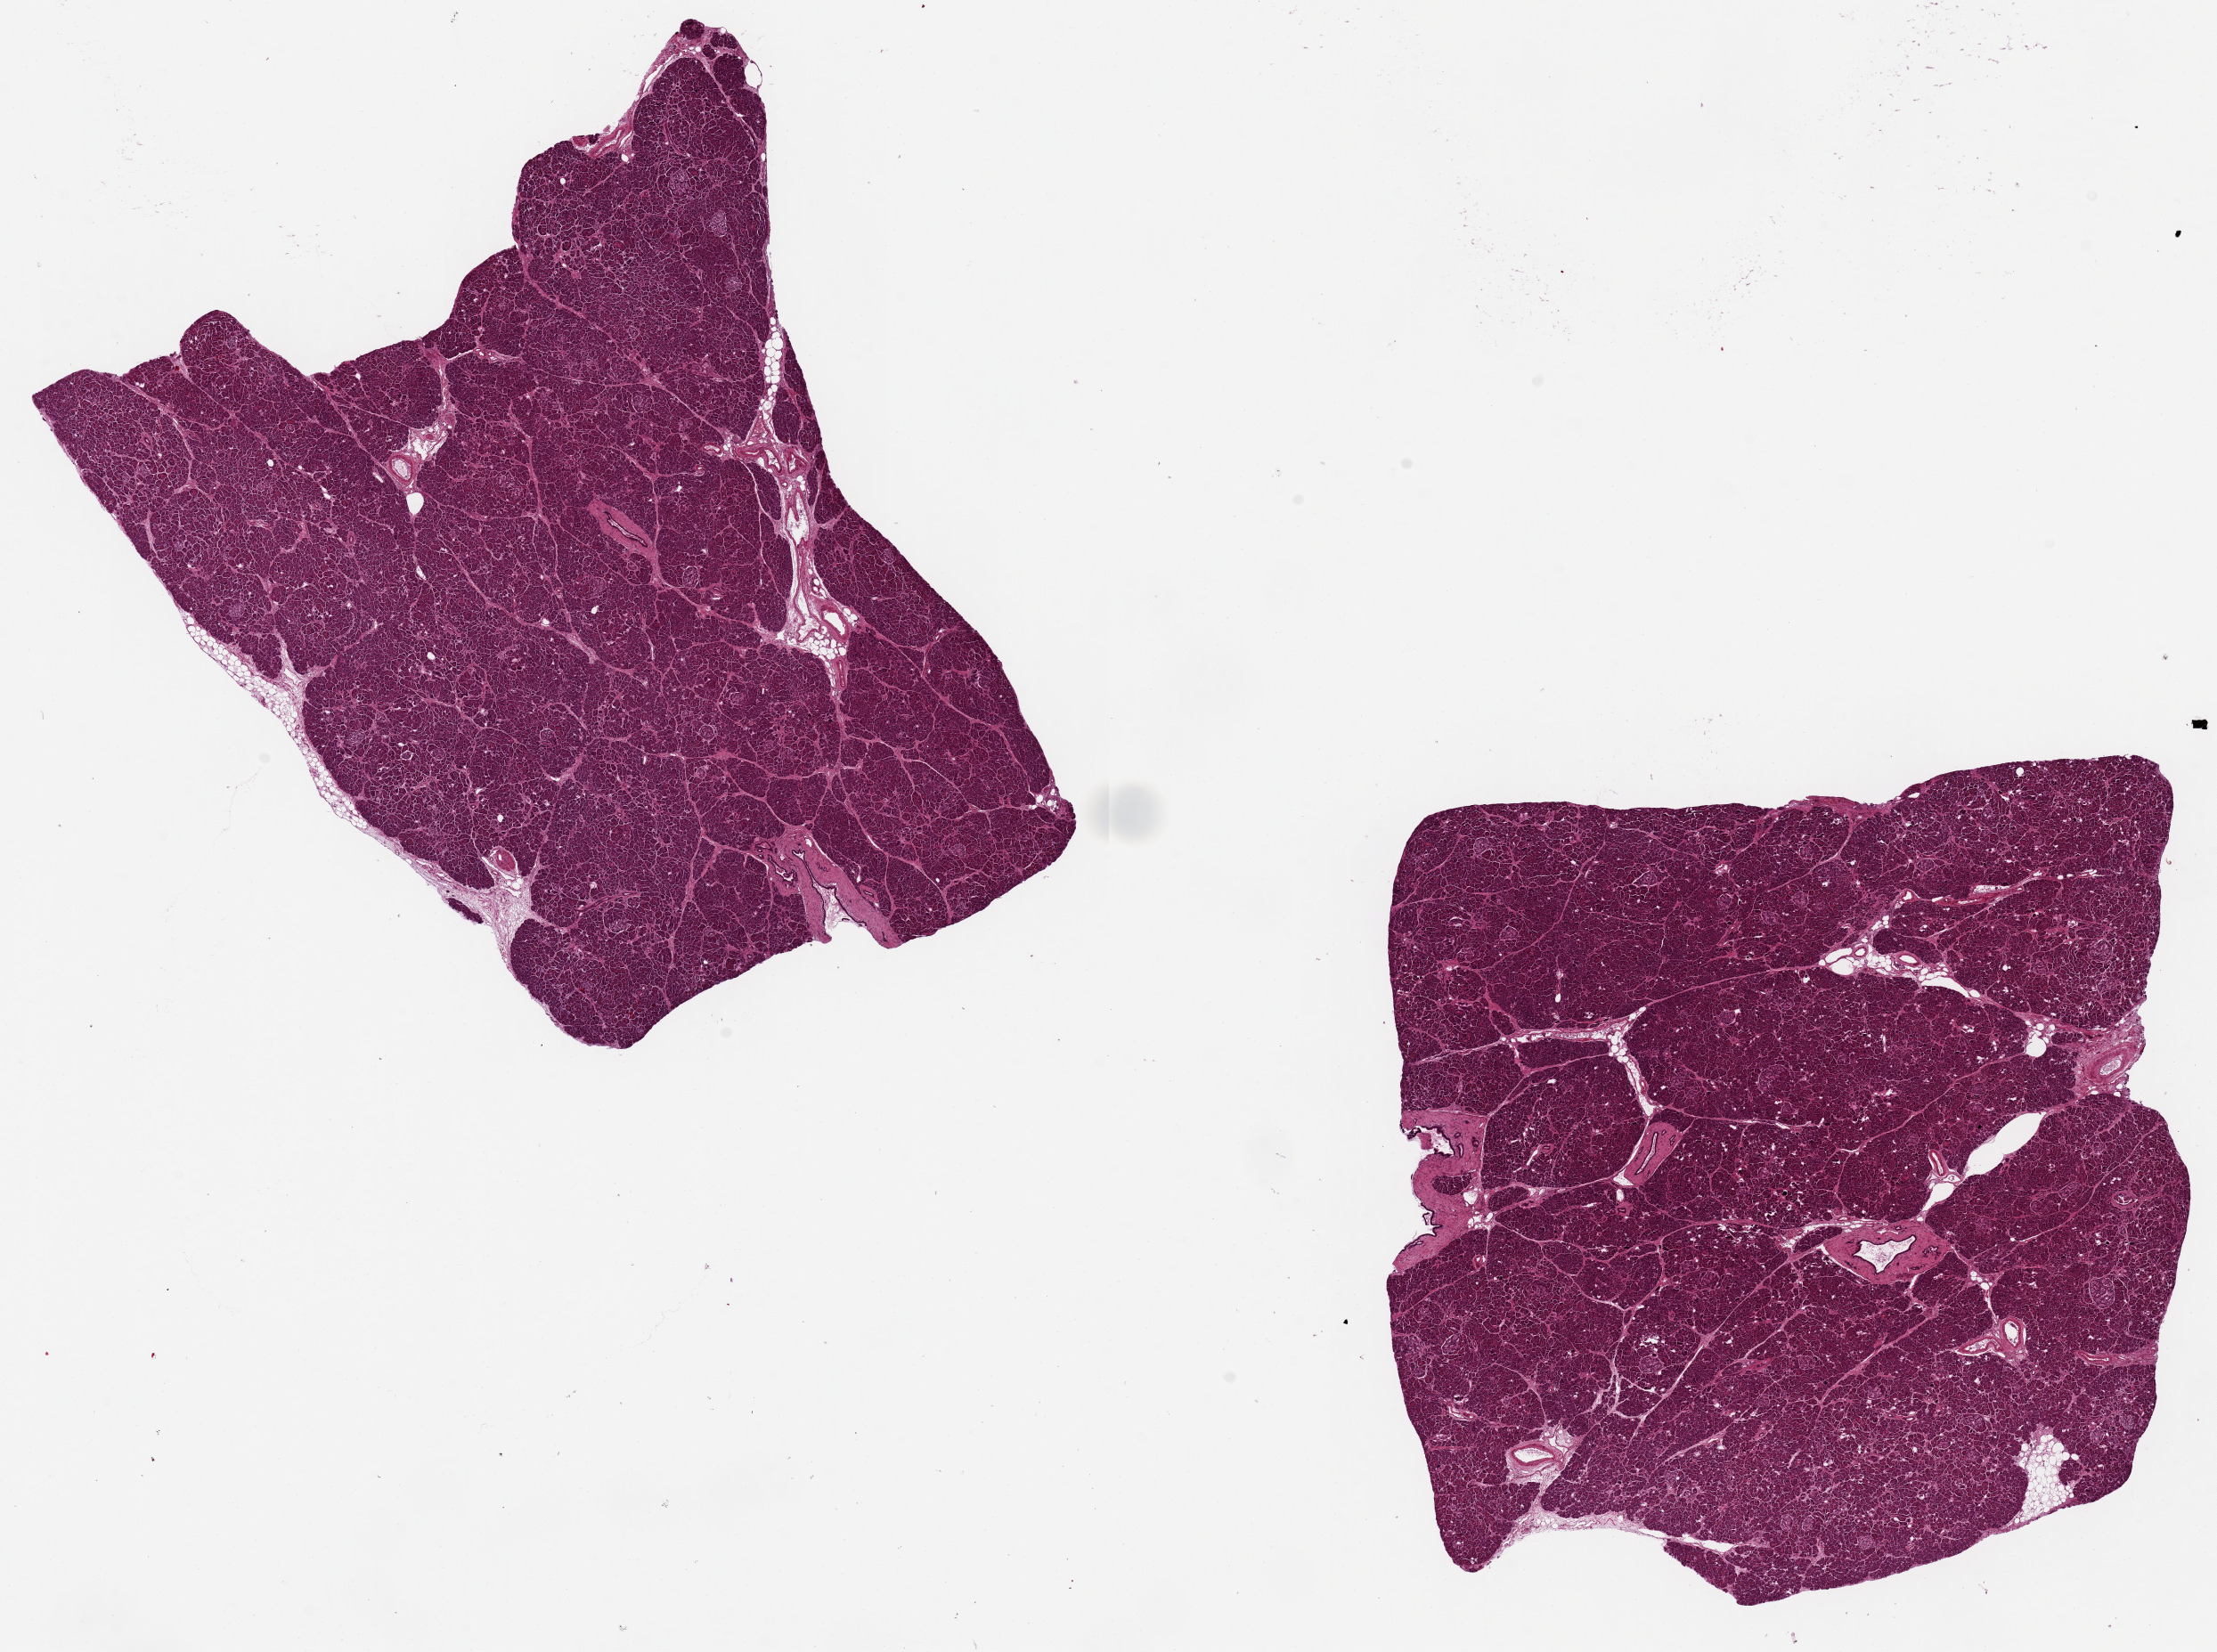
Whole-slide image, haematoxylin and eosin stain, whole scanned area (about 19.7 x 14.7 mm) shown as a low-resolution overview, PAXgene-fixed paraffin-embedded (PFPE) section, target tissue: pancreas, tissue donor sample. Donor: female.
• review note (as recorded): 2 pieces, ~8x7mm, remarkably well-preserved; Islets well-visualized and numerous